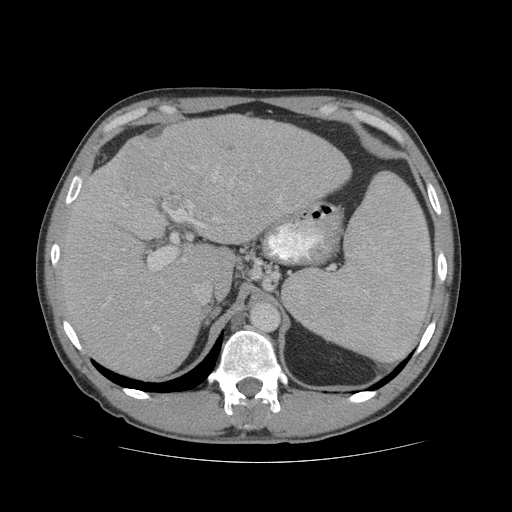
Contrast-enhanced abdominal CT (liver protocol), one axial slice. Slice 46 of 81 in the series (ordered by position). Reconstruction kernel STANDARD. 140 kVp. Soft-tissue window (W 400 / L 40 HU). 2.5 mm slice thickness. 512 × 512 image matrix, field of view 400 × 400 mm. Case-level facts recorded for this patient, not image findings: diagnosis: hepatocellular carcinoma (patient treated with transarterial chemoembolisation; whether this scan precedes or follows treatment is not stated here); TNM stage (as recorded): Stage-IVB; Child-Pugh class: B; tumour differentiation: well differentiated; tumour nodularity: multinodular.
Outlined on this slice (semi-automatic segmentation, software-assisted and operator-edited):
- liver parenchyma outside the tumour (the mass and vessels are separate outlines, so this box may not span the whole liver): bounding box [x1, y1, x2, y2] px = [58, 114, 350, 378]
- mass: [113, 141, 221, 207]
- liver vessels: [98, 167, 282, 330]